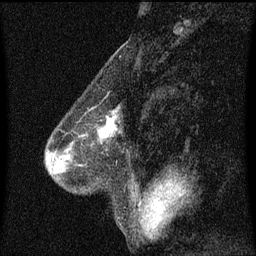
Breast MRI (dynamic contrast-enhanced), one sagittal slice. Slice 29 of 60 in the series (ordered by position). Dynamic contrast-enhanced series, image 2 of 3 at this slice position (ordered by acquisition). 1.5 T. TE 4.2 ms, TR 8.4 ms. 2 mm slice thickness. 256 × 256 image matrix. Patient: female, 58 years.
Structures marked on this image (semi-automatic segmentation, software-assisted and operator-edited):
- analysis volume of interest (the breast-tissue region the enhancement analysis was run in; not a lesion): bounding box [x1, y1, x2, y2] px = [79, 108, 121, 143]
- tumour enhancement mask (voxels above the 70 % enhancement threshold inside the analysis volume of interest): [99, 118, 117, 139]